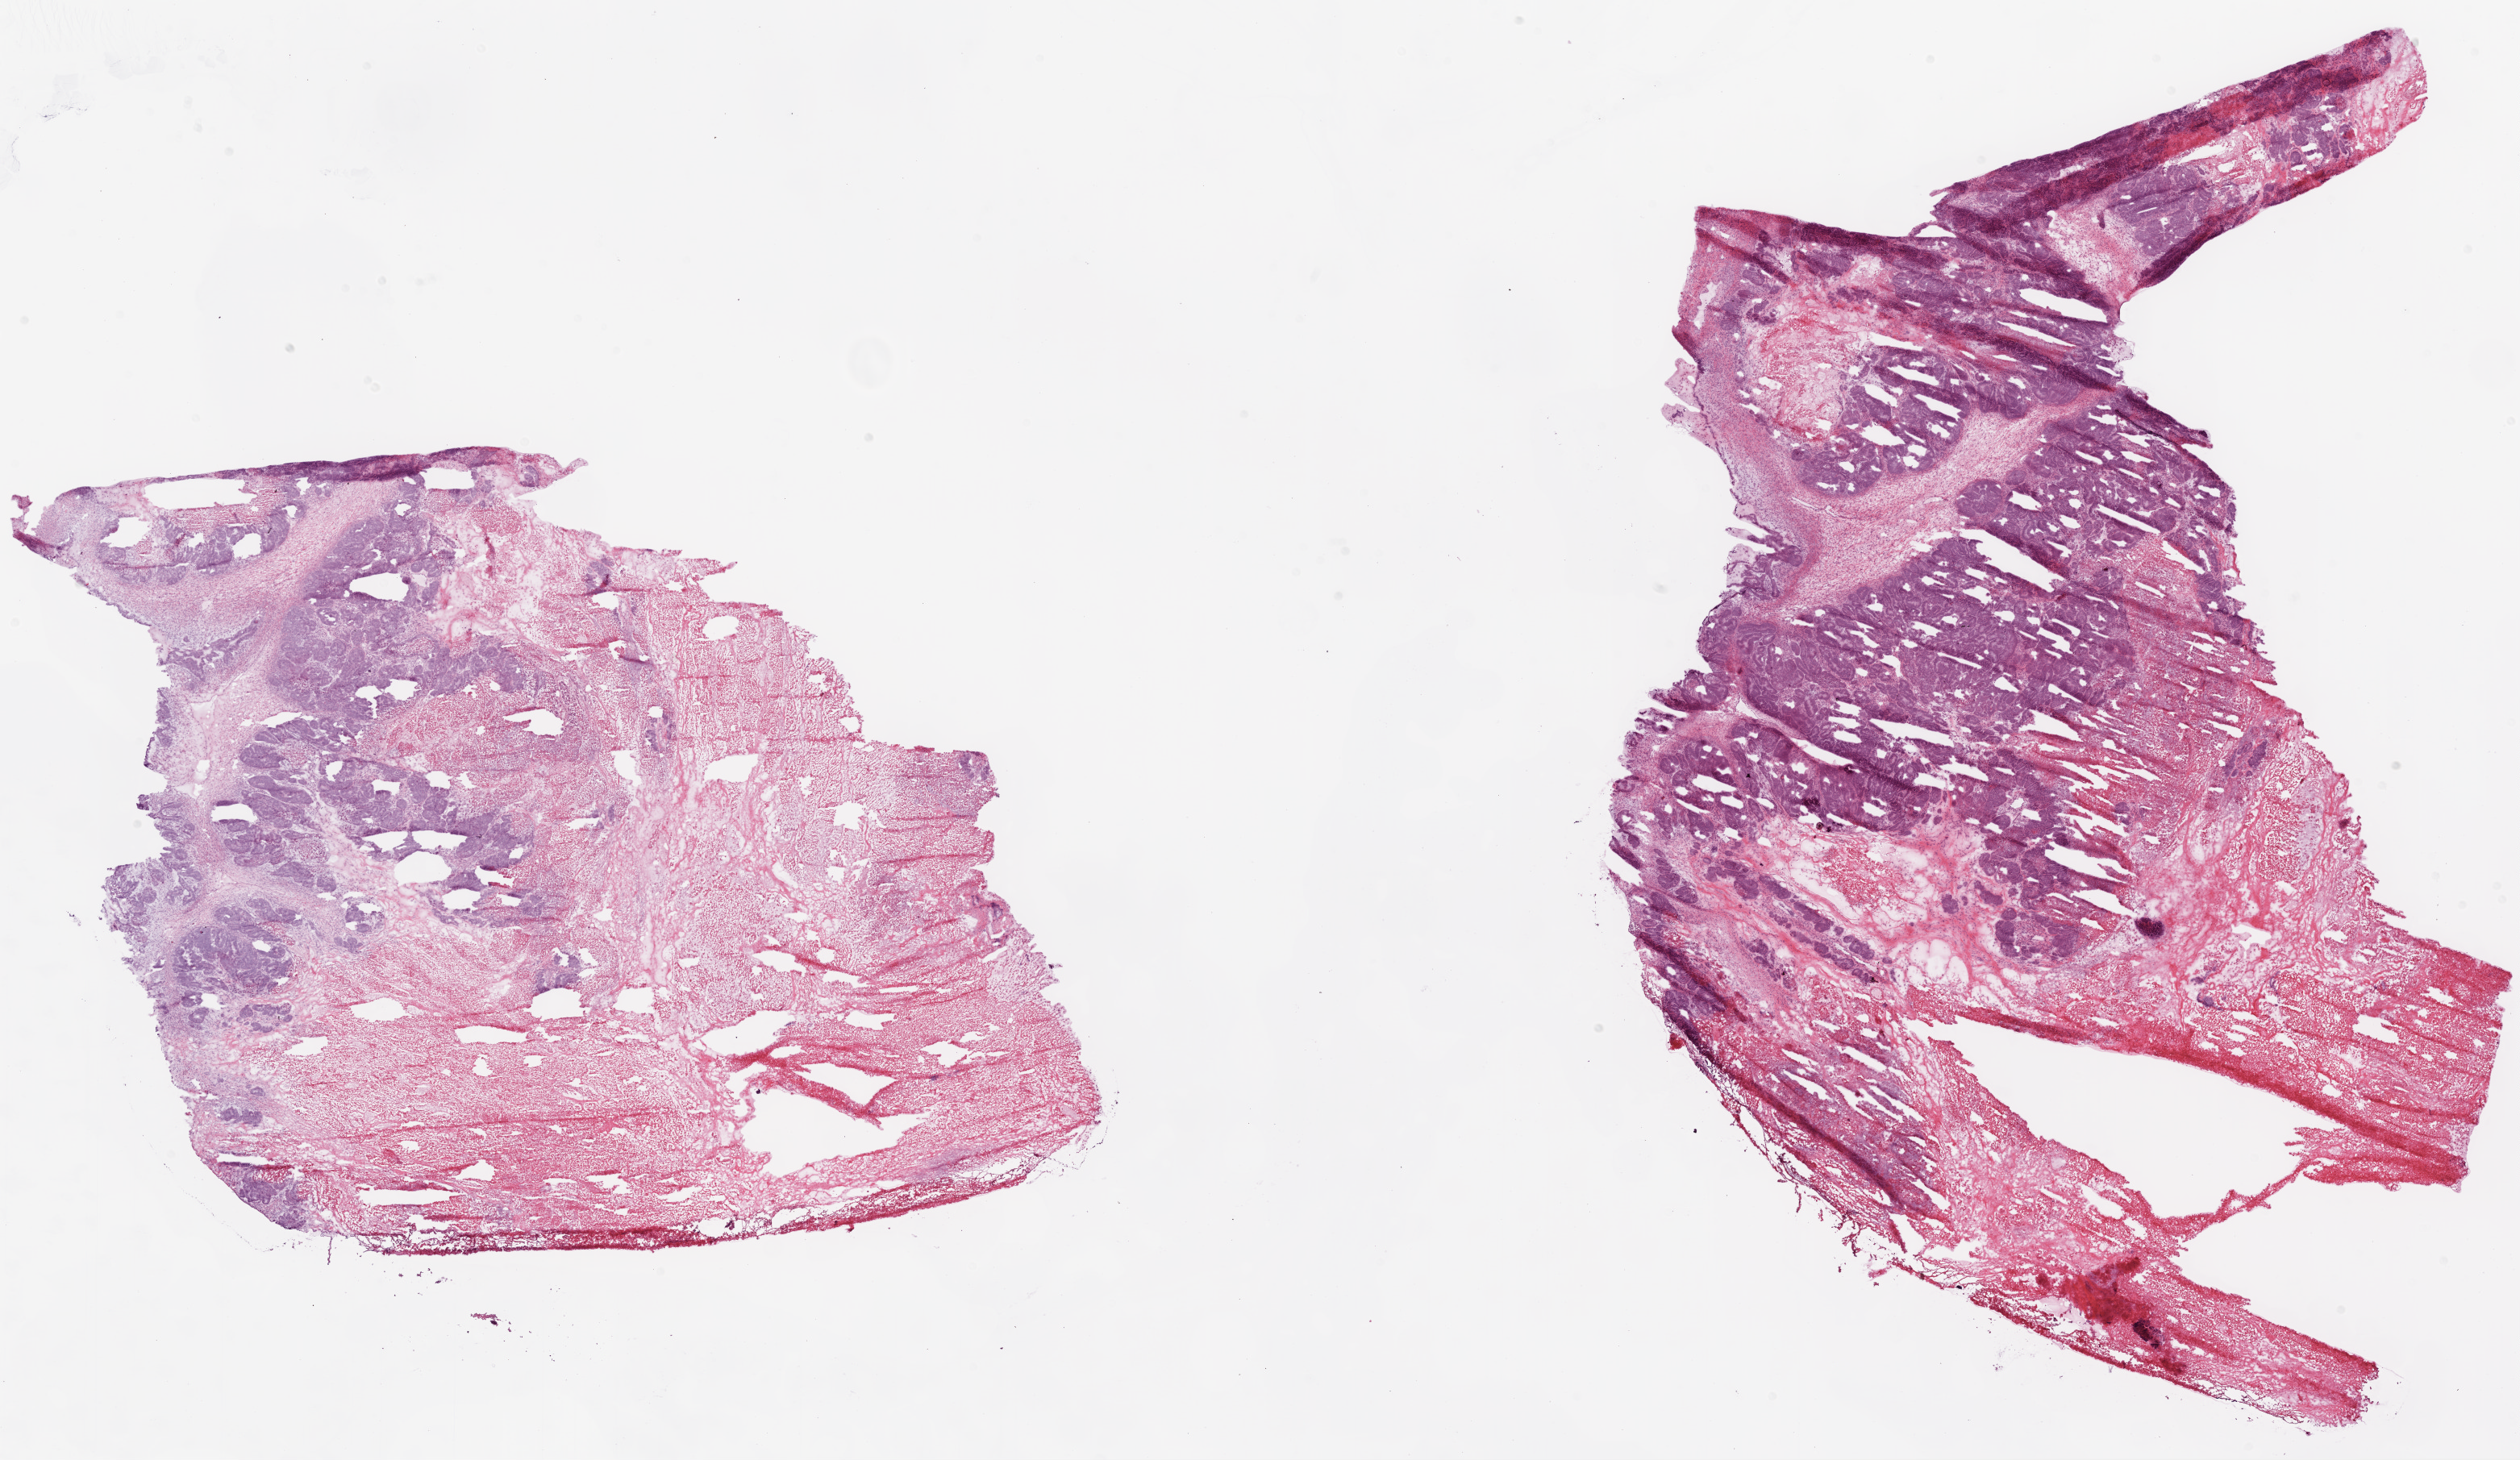
Whole-slide histology image, H&E-stained, shown as a low-resolution overview of the whole scanned area (about 25.1 x 14.5 mm, acquisition: 20x scan). Frozen section from the top of the tissue portion. Primary tumour sample from the ovary. Patient: female, age at initial diagnosis 43 years. Histologic grade: G2 (moderately differentiated). Slide review estimates, as recorded: tumour cells 45%, tumour nuclei 70%, normal cells 0%, stromal cells 50%, necrosis 5%.
Diagnosis: Serous cystadenocarcinoma, NOS. FIGO stage: IIC.